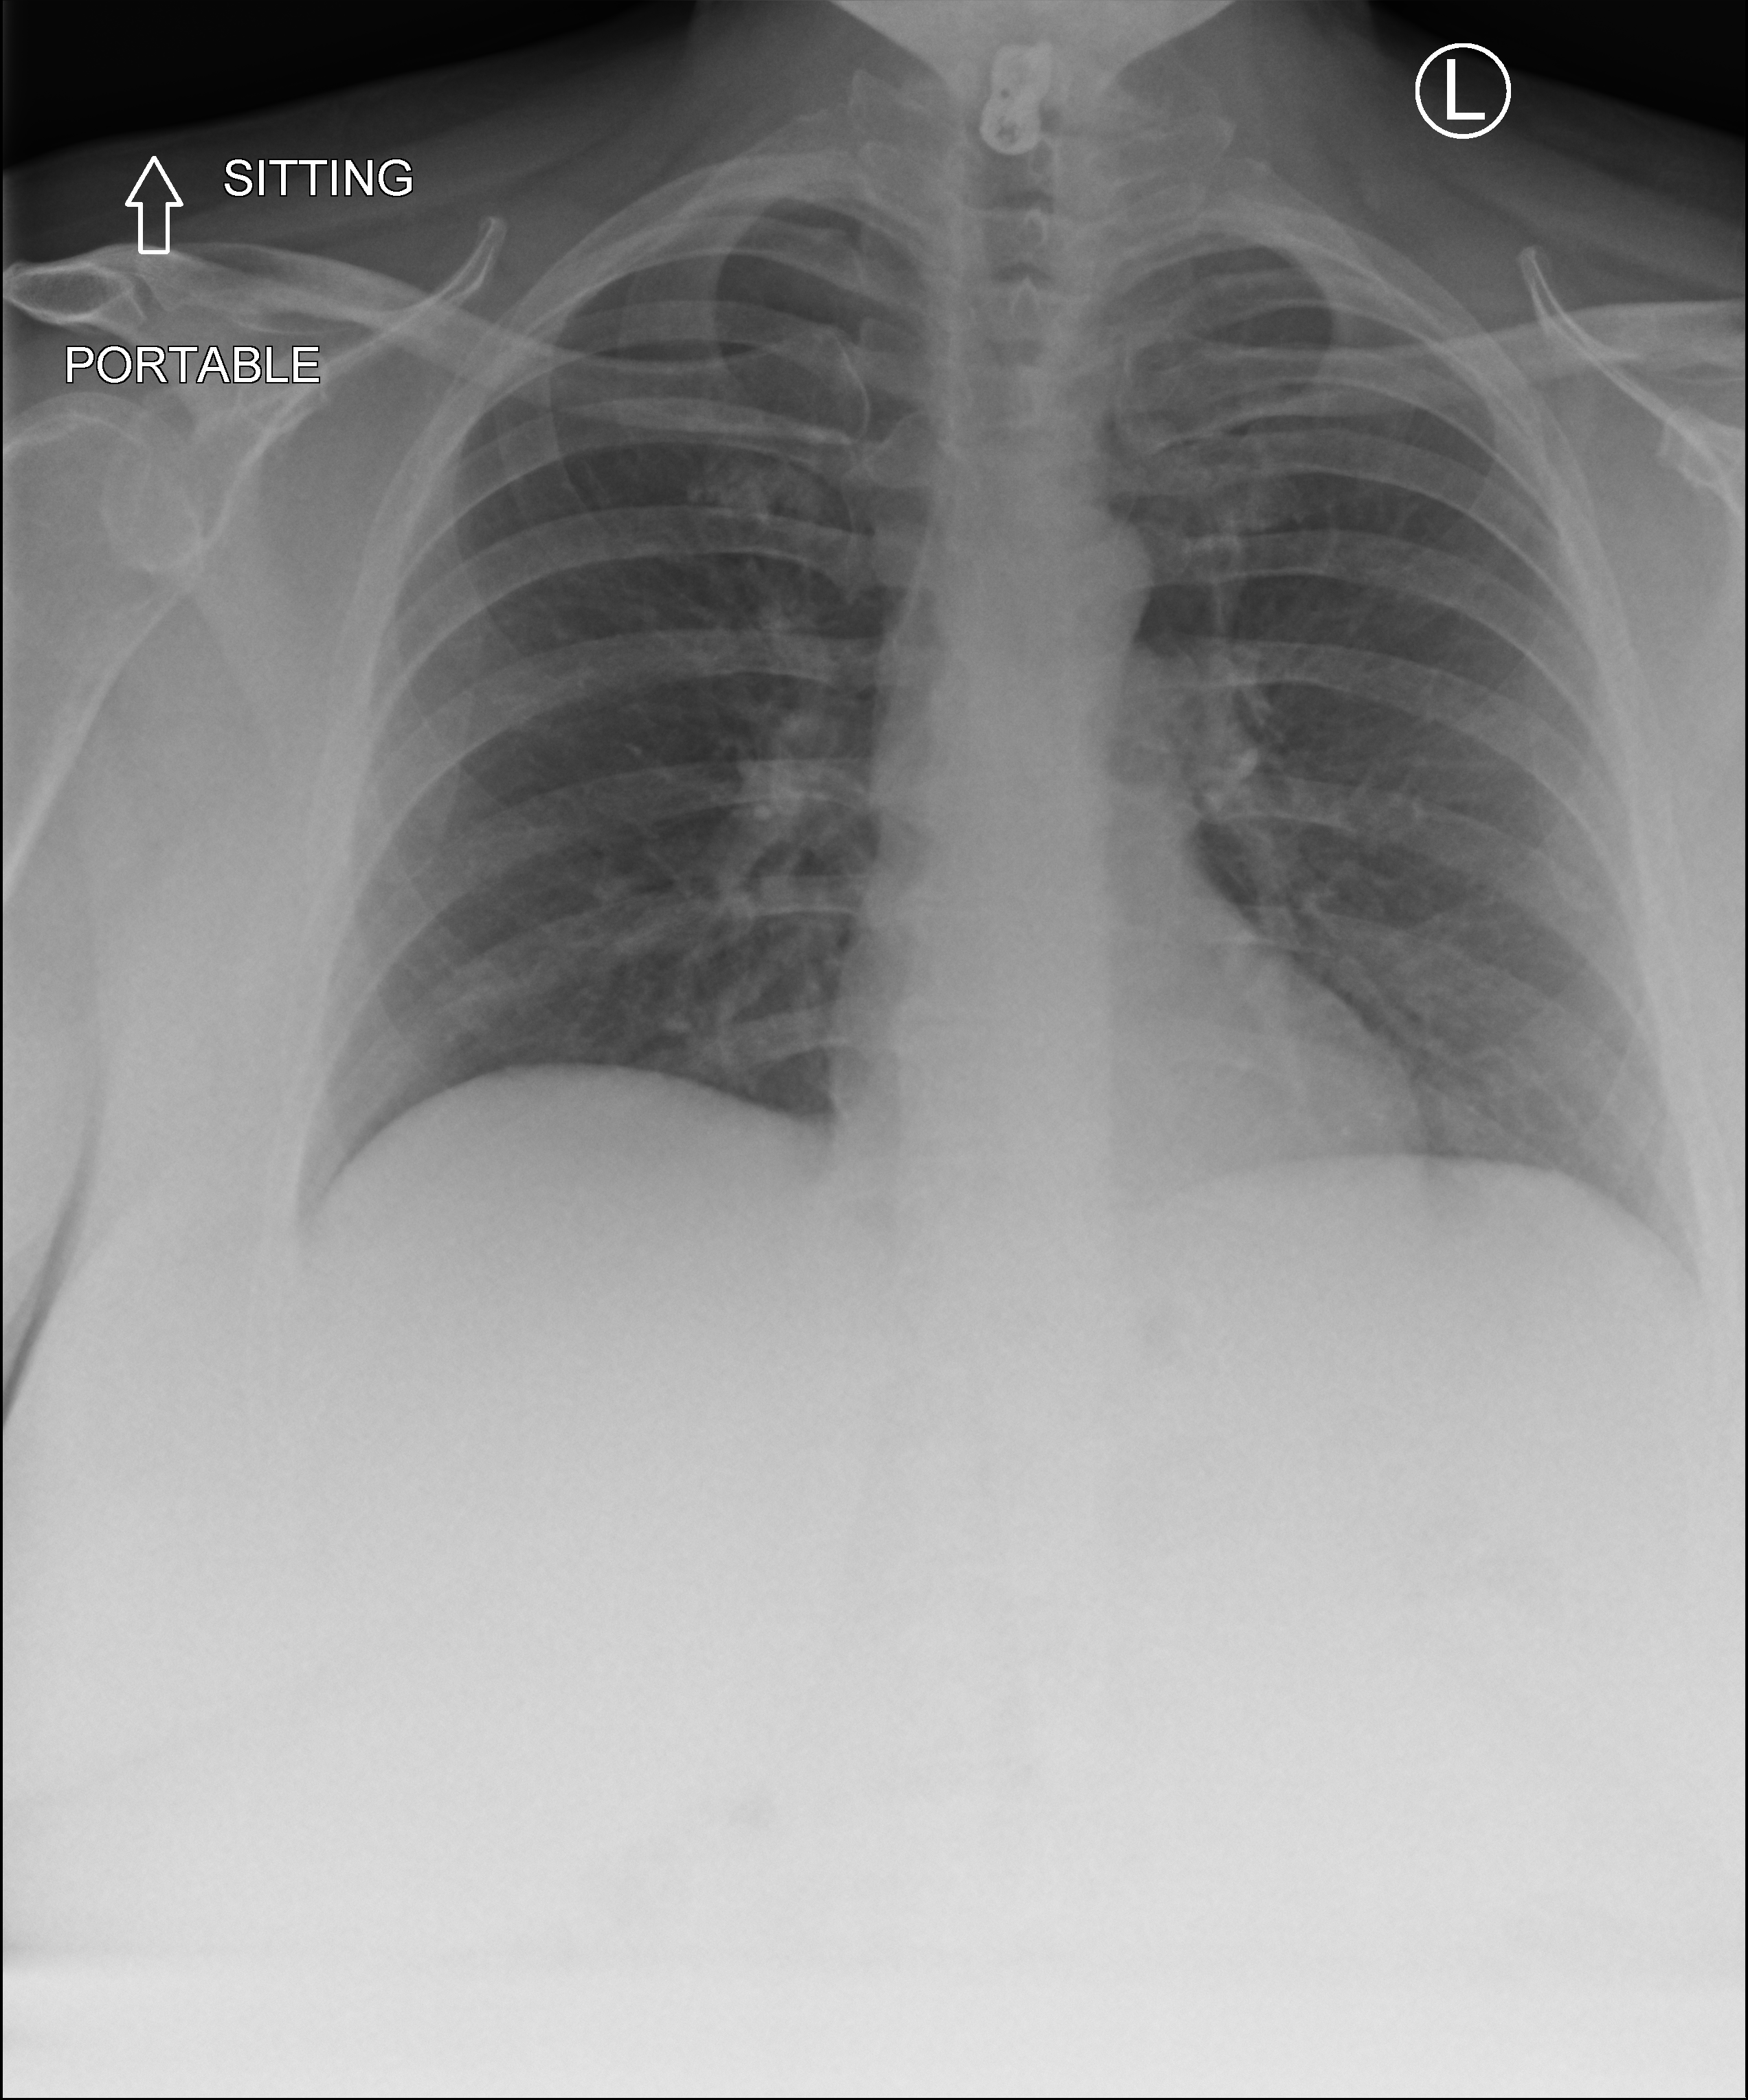
Portable chest radiograph, anteroposterior (AP) projection. Female patient hospitalised with COVID-19, age 18–59 years.
From the hospital-stay record, not from the radiograph (when in the stay this image was taken is not recorded): hypertension (admission record): yes.